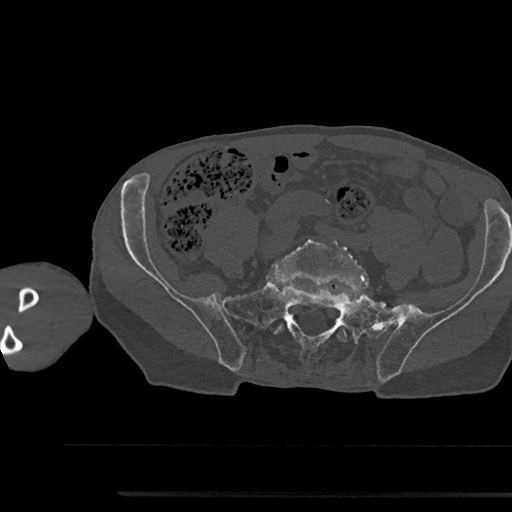
CT including the spine, one axial slice; reconstruction kernel Br40s/3; bone window (W 1800 / L 400 HU); 0.5 mm slice thickness; 512 × 512 image matrix. Patient: male, 79 years. From the clinical record (not read from this slice): primary cancer: prostate.
Annotated regions visible in this slice (semi-automatic segmentation, software-assisted and operator-edited):
- L5 vertebra: bounding box [x1, y1, x2, y2] px = [274, 235, 368, 342]